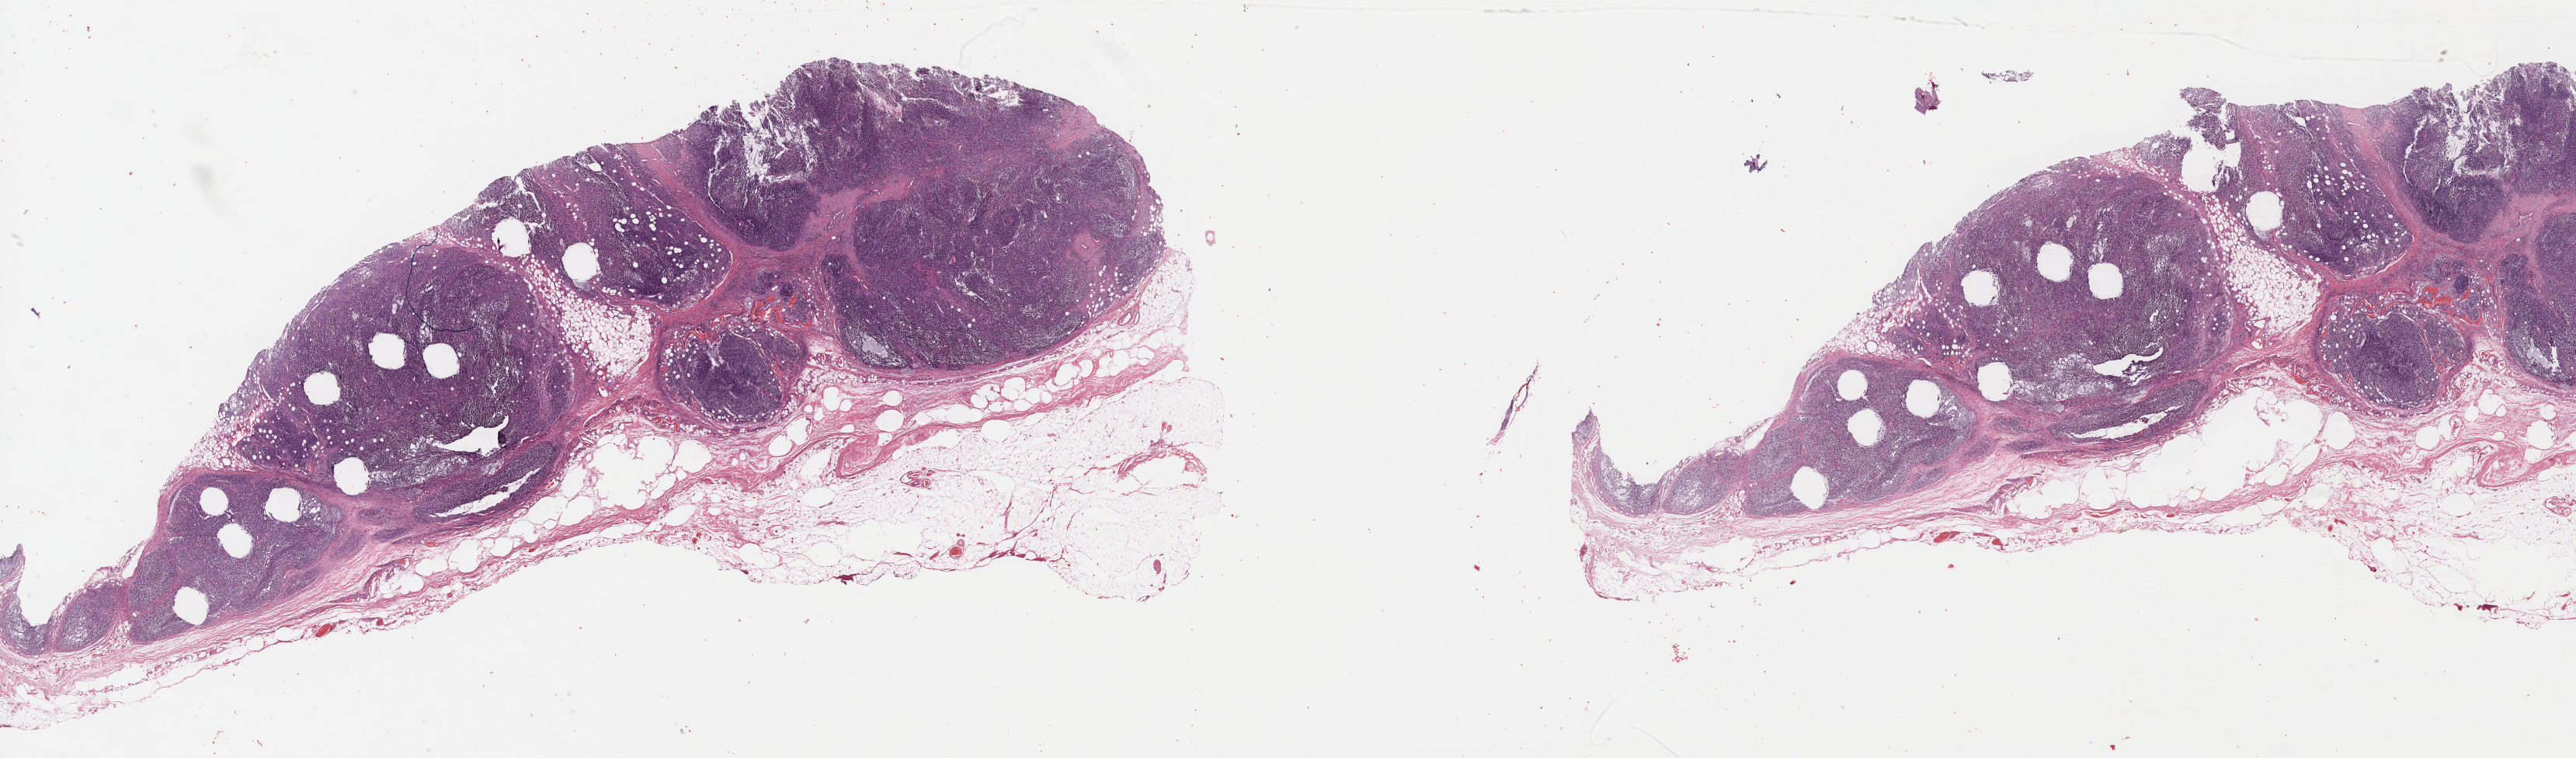
H&E-stained whole-slide image — low-resolution overview of the scanned area, about 52.1 x 15.3 mm (slide scanned at 40x). Formalin-fixed paraffin-embedded (FFPE) diagnostic section. Metastatic tumour sample, sampled site: lymph node. Male, age 63 years at initial diagnosis.
• this section: metastatic tumour tissue
• patient diagnosis: Malignant melanoma, NOS